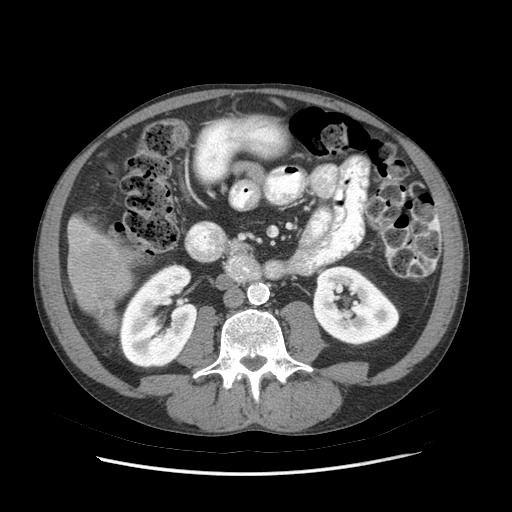
Contrast-enhanced abdominal CT (liver protocol), one axial slice. Position 16 of 89 along the scan axis. Reconstruction kernel STANDARD. 140 kVp. Soft-tissue window (W 400 / L 40 HU). 2.5 mm slice thickness. 512 × 512 image matrix, field of view 380 × 380 mm. From the clinical record (not read from this slice): diagnosis: hepatocellular carcinoma (patient treated with transarterial chemoembolisation; whether this scan precedes or follows treatment is not stated here); TNM stage (as recorded): Stage-IIIB; Child-Pugh class: A; tumour differentiation: moderately differentiated.
Outlined on this slice (semi-automatic segmentation, software-assisted and operator-edited):
- liver parenchyma outside the tumour (the mass and vessels are separate outlines, so this box may not span the whole liver): box from (x=68, y=216) to (x=136, y=330) px